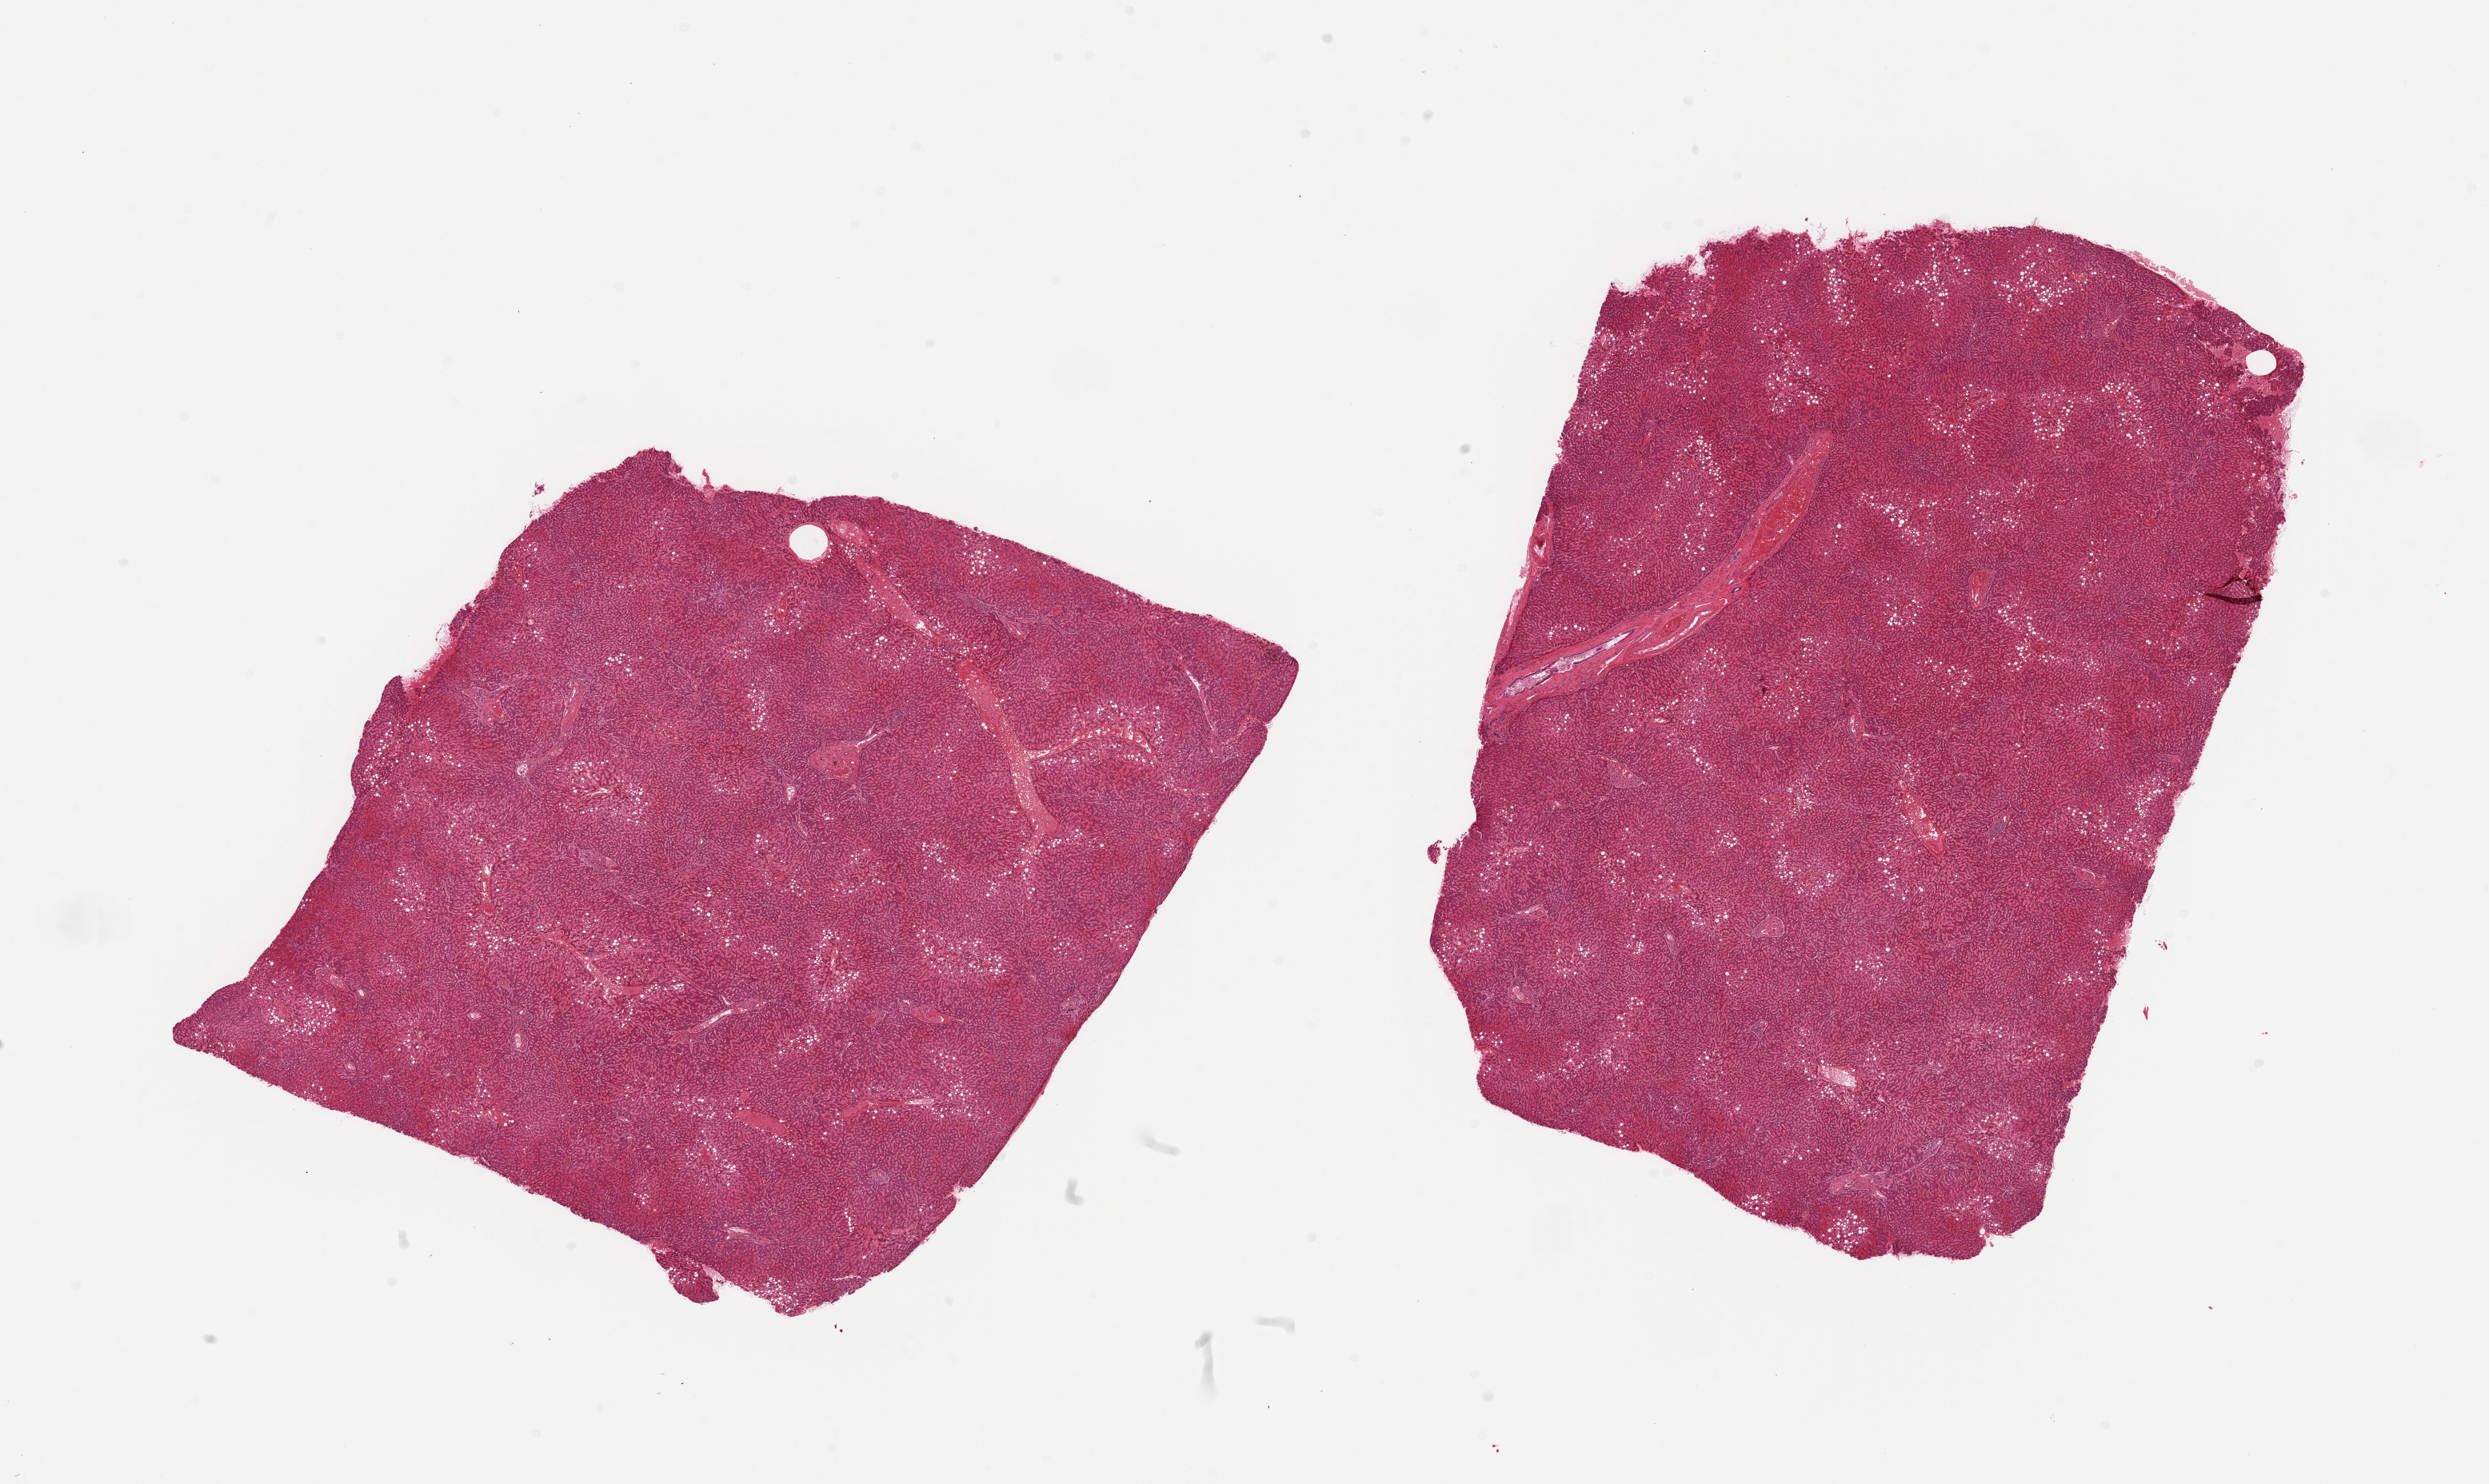
H&E whole-slide image, brightfield — a low-resolution overview of the entire scanned area, about 24.6 x 14.7 mm. PAXgene-fixed, paraffin-embedded tissue. Section of liver (target tissue). Donor tissue sample. Donor: male.
Review note (as recorded): 2 pieces, centrilobular macrovesicular steatosis involves ~20-30% of parenchyma.